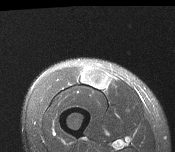
MRI of an extremity soft-tissue mass, one axial slice; slice 43 of 116 in the series (ordered by position); T2-weighted fat-saturated; MR volume resampled by the dataset authors to the PET/CT grid (not the native acquisition matrix); 3.27 mm slice thickness; 175 × 152 image matrix, field of view 171 × 148 mm. Male patient. Case-level facts recorded for this patient, not image findings: histological type: pleiomorphic leiomyosarcoma; grade: intermediate; site of the primary tumour: right thigh.
Outlined on this slice (expert contour drawn on MRI and transferred to this co-registered scan by the dataset authors):
- gross tumour volume including surrounding oedema: bounding box (x1, y1, x2, y2) in pixels: (81, 70, 109, 89)